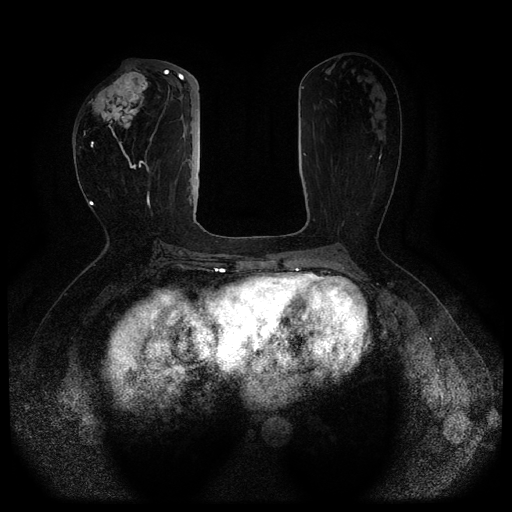
Breast MRI (dynamic contrast-enhanced, multi-phase), one axial slice. Position 40 of 116 along the scan axis. Dynamic contrast-enhanced series, time point 2 of 5 at this slice position (early post-contrast). 1.5 T. TE 2.6 ms, TR 5.3 ms. 2 mm slice thickness. 512 × 512 image matrix, field of view 350 × 350 mm. Female patient, age 51 years.
Annotated regions visible in this slice (semi-automatically segmented with operator editing):
- breast lesion (labelled 'tumour' in the annotation; benign lesions carry a separate 'benign' label): bounding box [x1, y1, x2, y2] px = [89, 67, 149, 129]